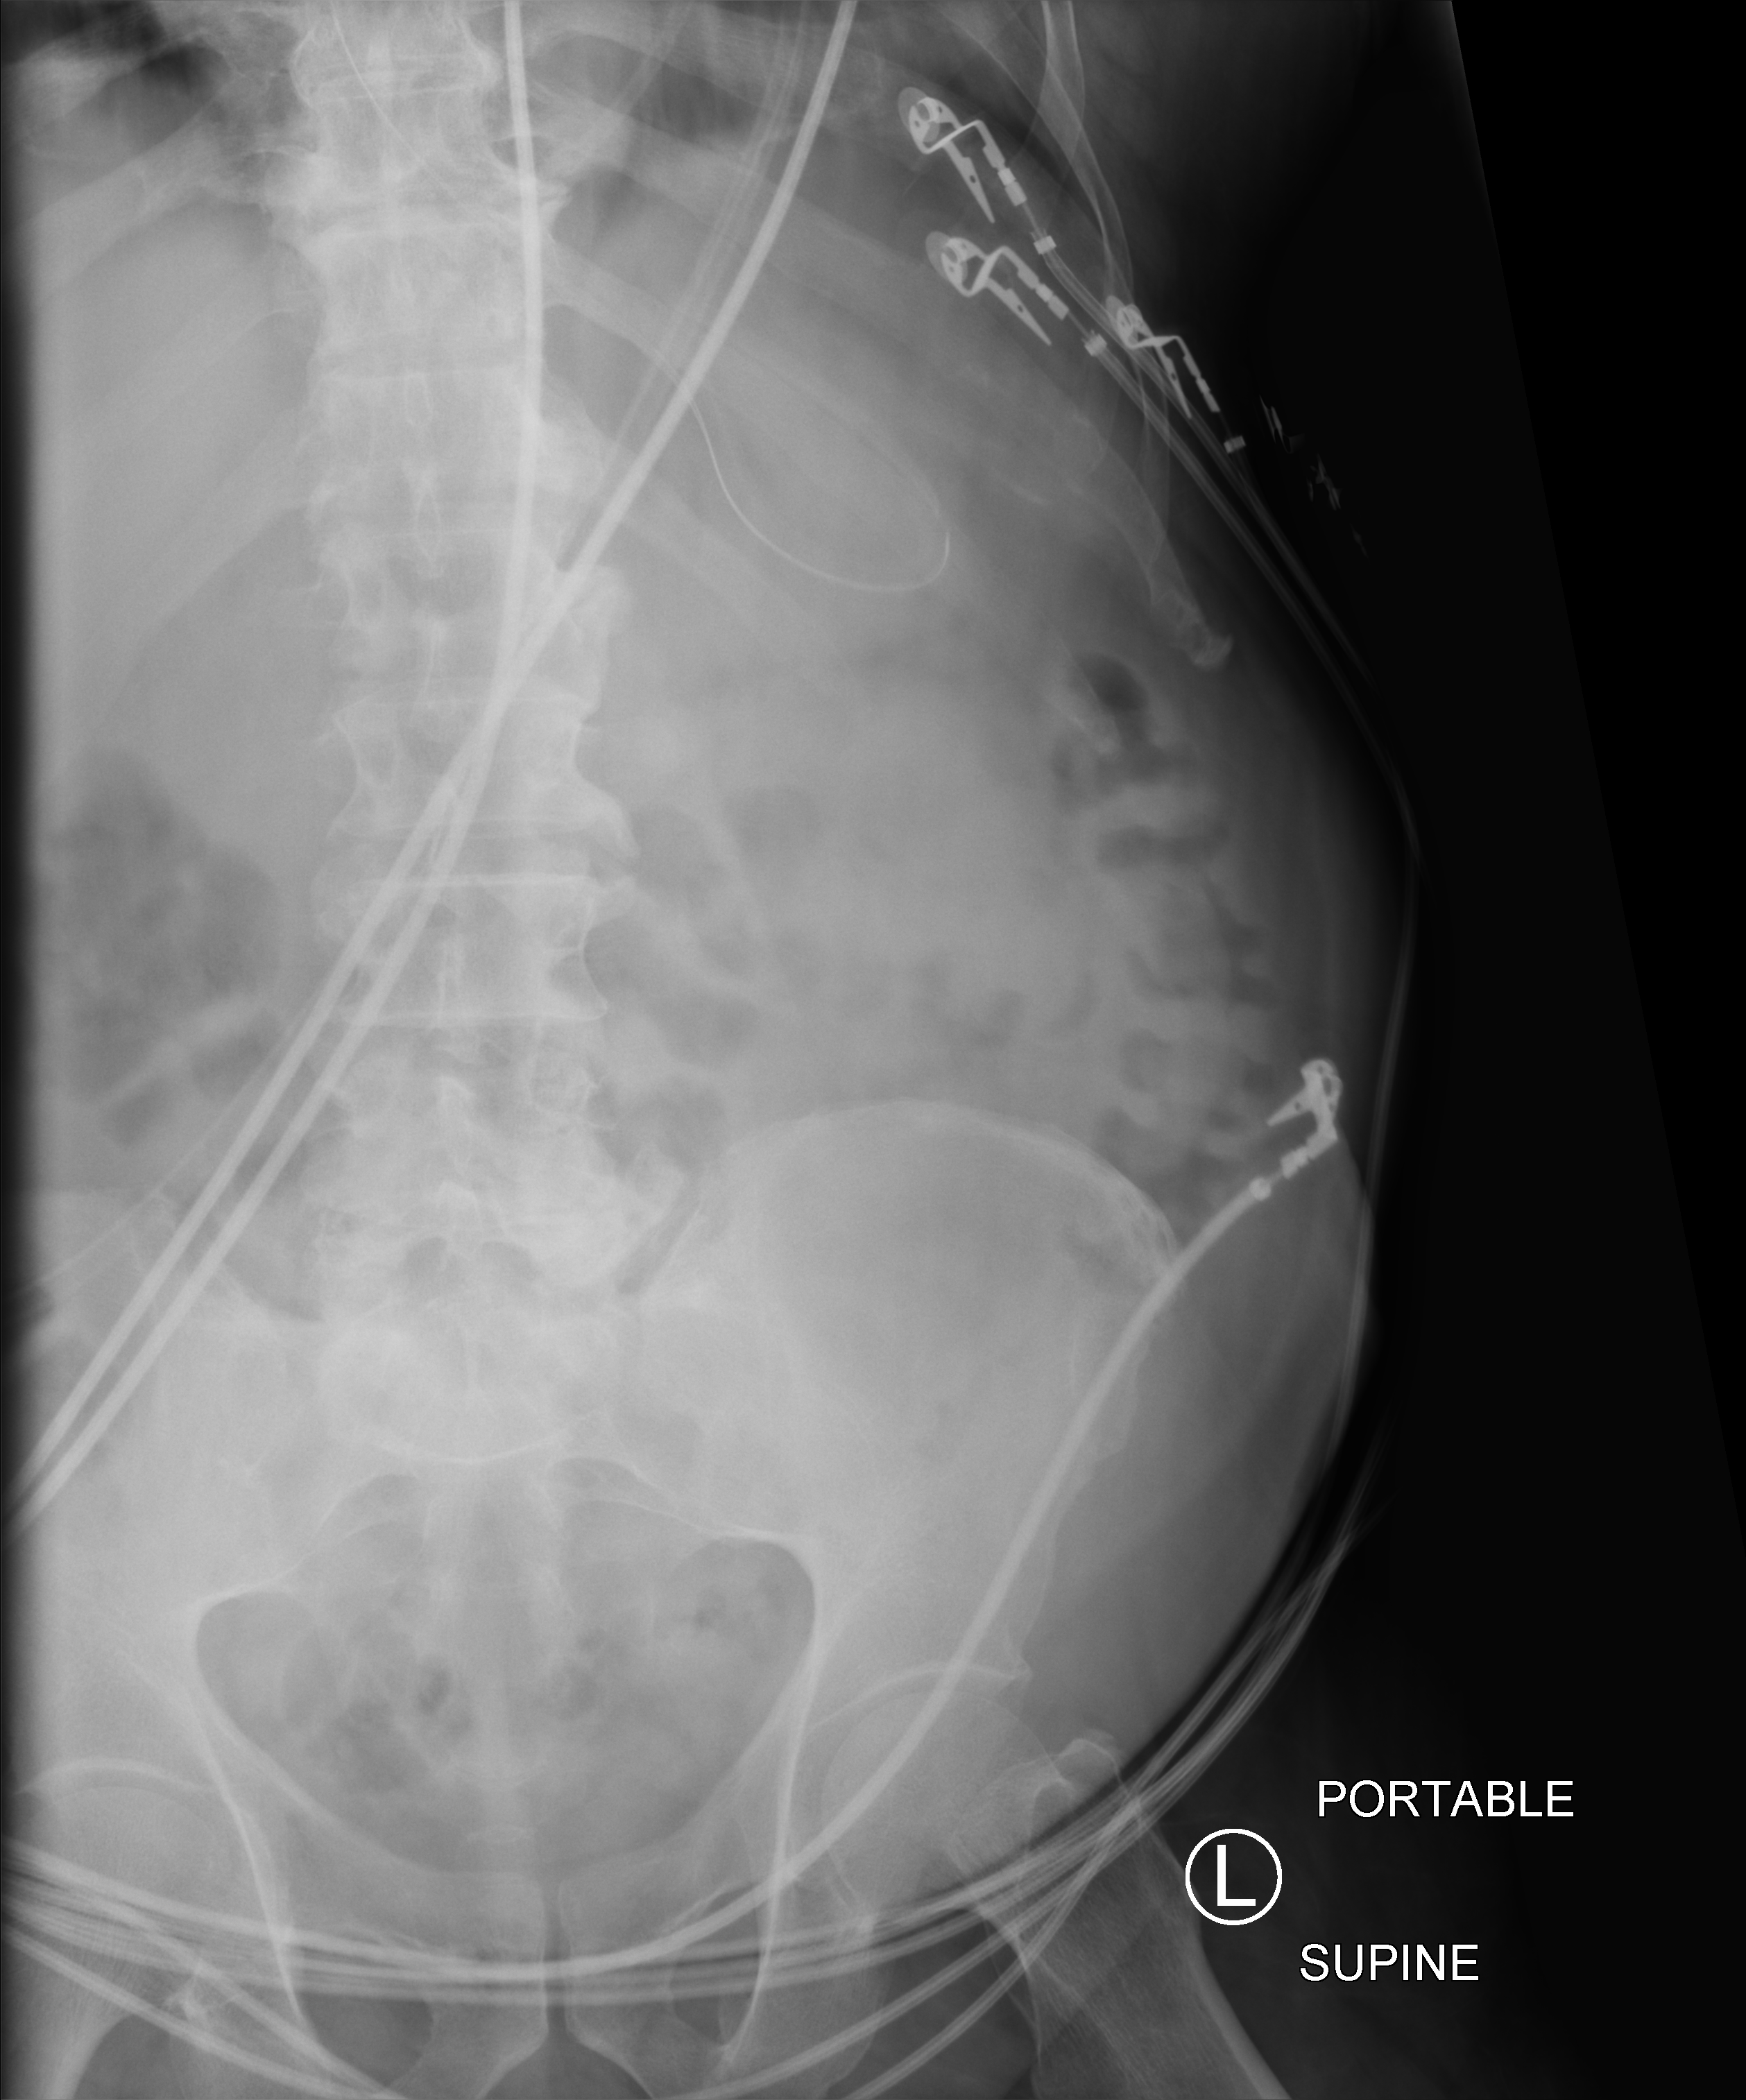
Portable abdomen radiograph, anteroposterior (AP) projection. Patient hospitalised with COVID-19; male, aged 60–74 years.
From the hospital-stay record, not from the radiograph (when in the stay this image was taken is not recorded): mechanically ventilated during this hospital stay: yes; chronic kidney disease (admission record): no.